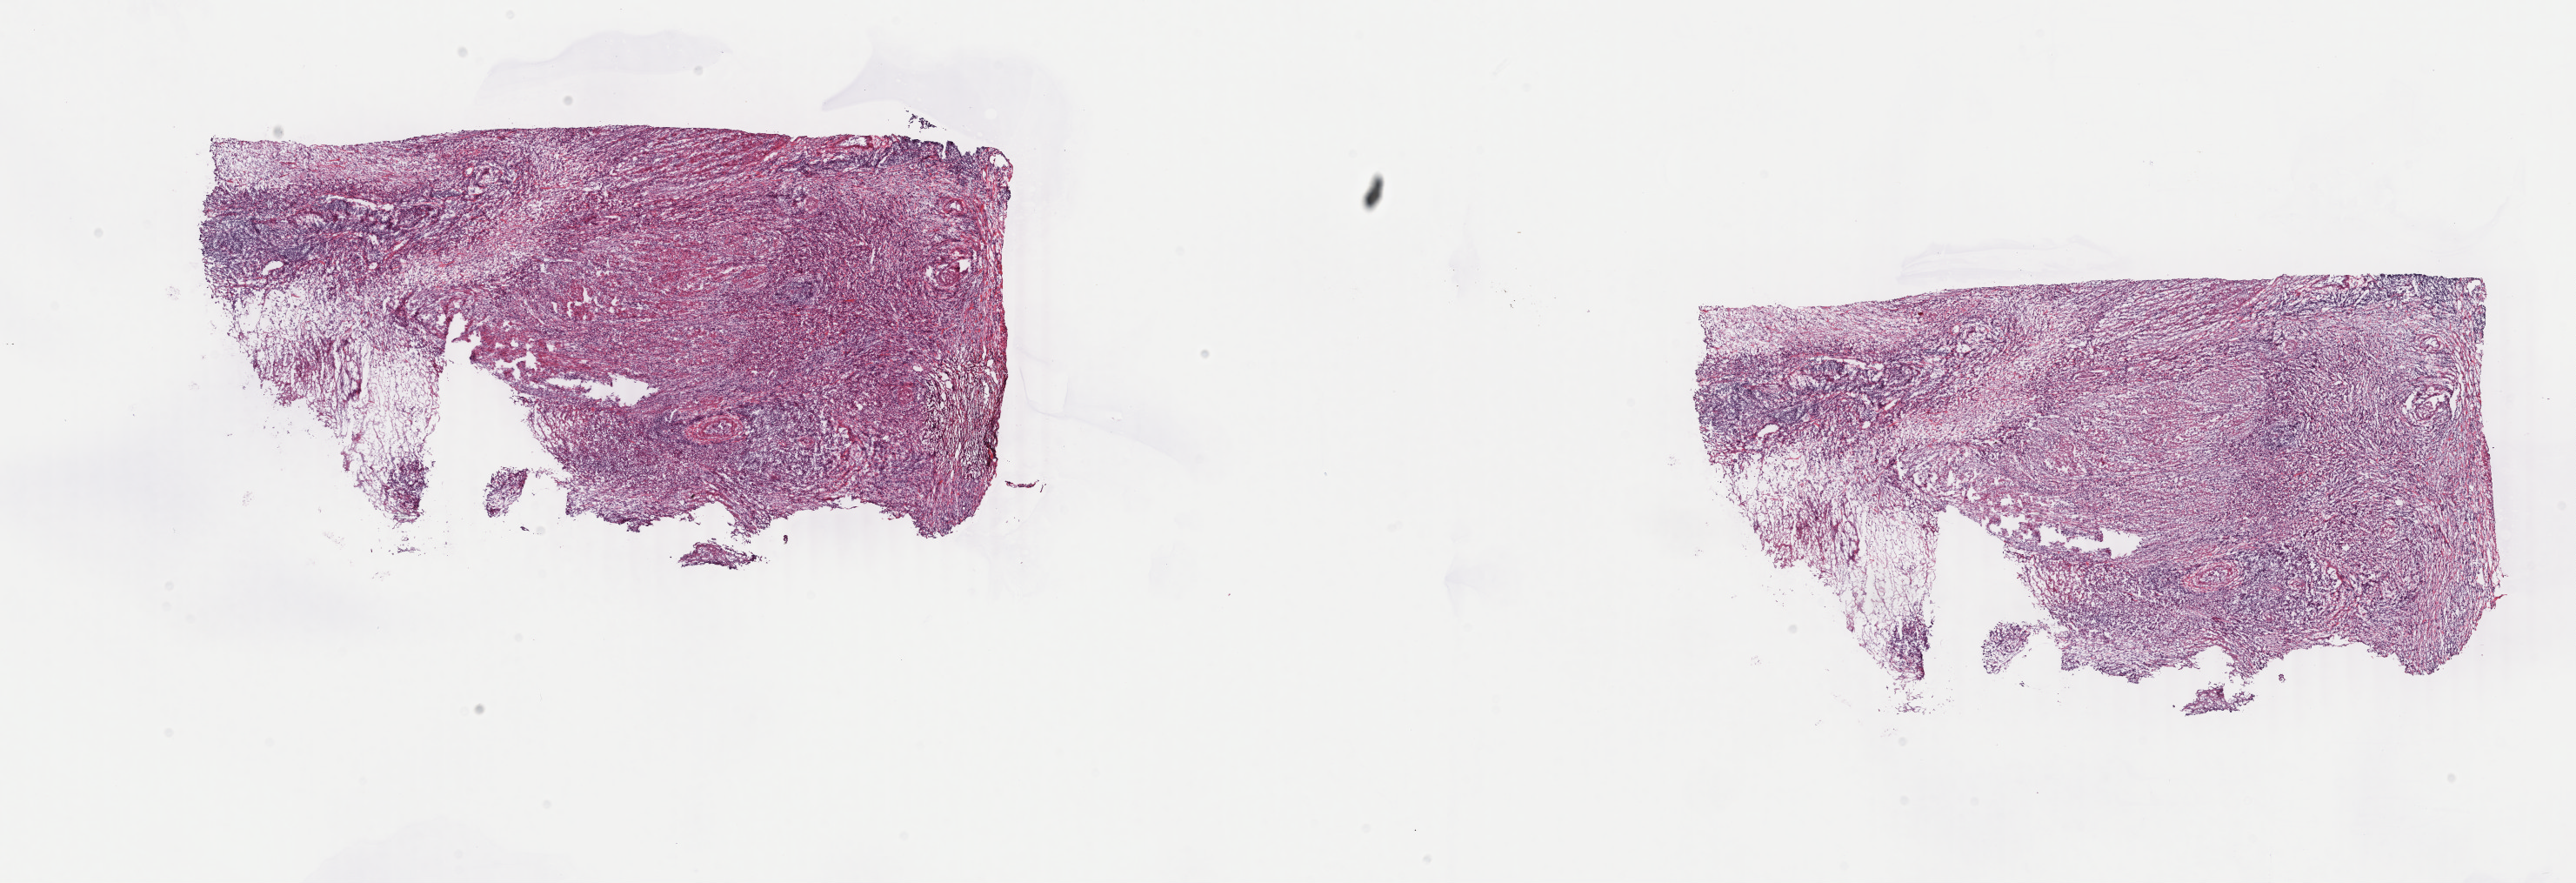
Digitized Hematoxylin and eosin (H&E) stained tissue section (whole slide) — shown as a low-resolution overview of the whole scanned area (about 23.6 x 8.1 mm, slide scanned at 40x), frozen section from the top of the tissue portion, sample: primary tumour, bladder. Patient: male, age at initial diagnosis 69 years. Histologic grade: high grade. Slide review estimates, as recorded: tumour cells 65%, tumour nuclei 65%, normal cells 0%, stromal cells 35%, necrosis 0%. Inflammatory infiltration, as recorded: lymphocyte infiltration 8%, monocyte infiltration 2%, neutrophil infiltration 4%.
- lymph nodes positive (case pathology): 0 of 27 examined
- AJCC pathologic stage: III (7th edition)
- diagnosis: Transitional cell carcinoma (lateral wall of bladder)